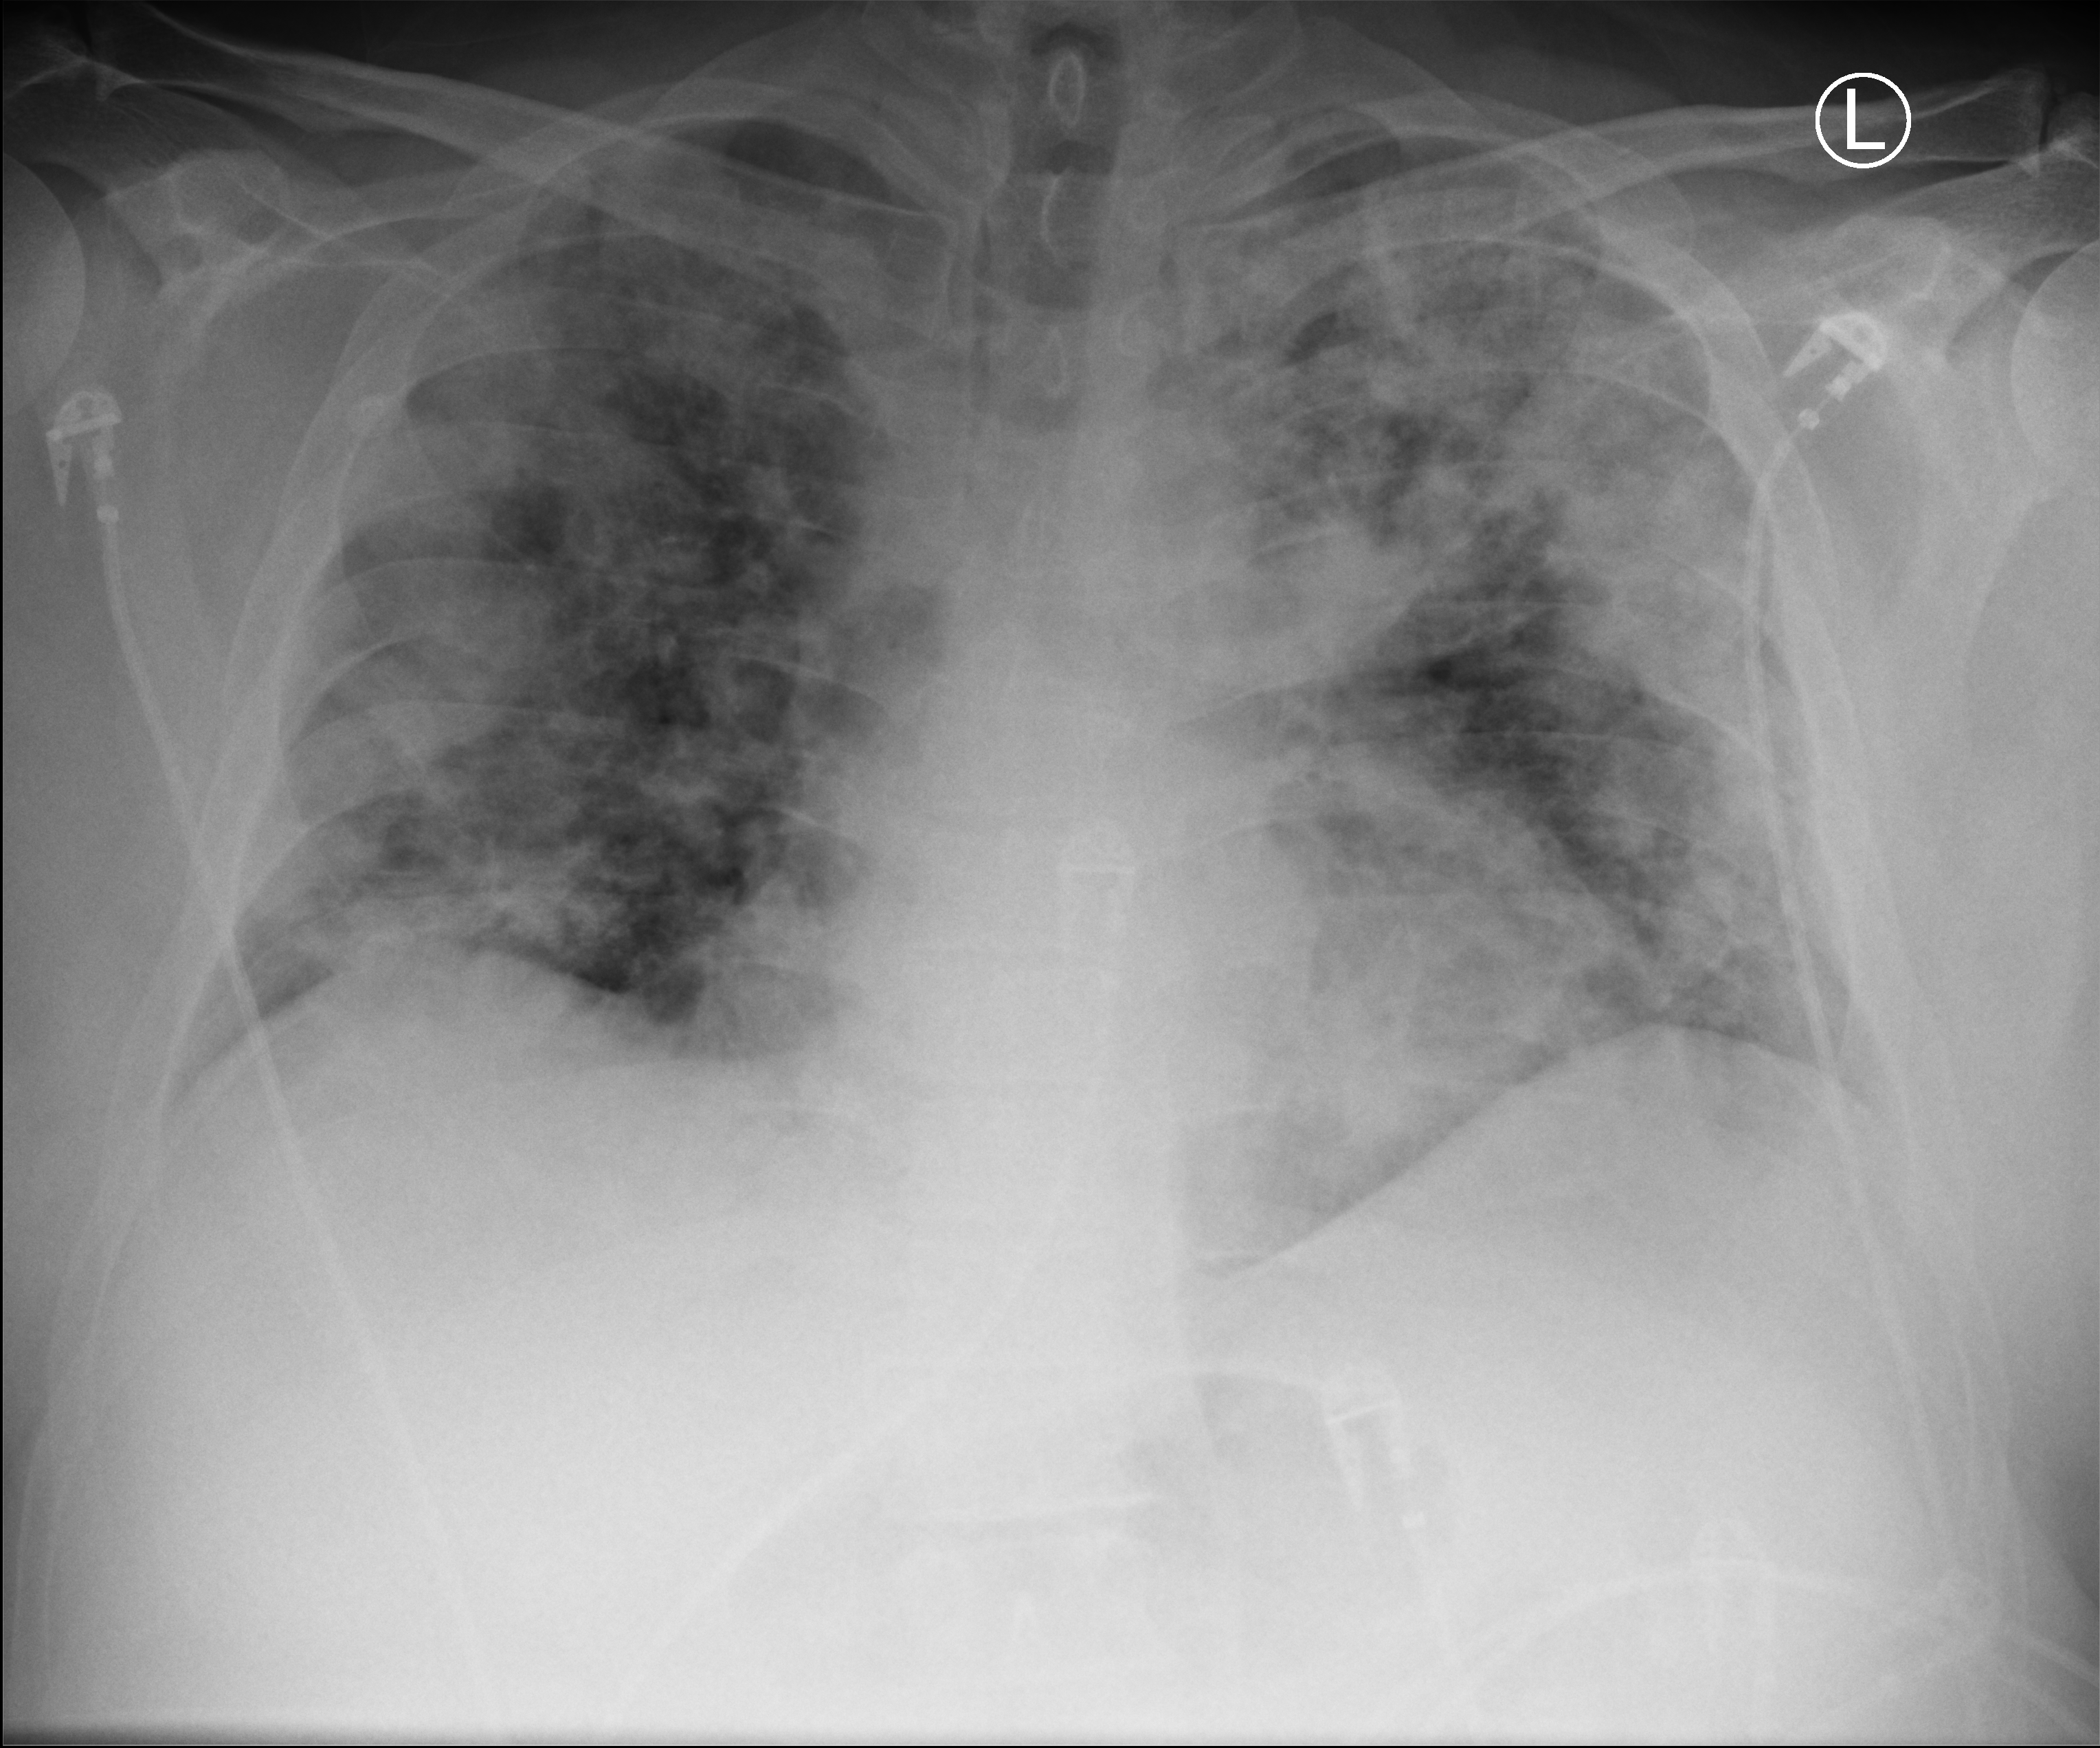
Bedside chest radiograph (computed radiography); anteroposterior (AP) projection. Male patient hospitalised with COVID-19, age 18–59 years.
From the hospital-stay record, not from the radiograph (when in the stay this image was taken is not recorded):
- length of hospital stay: 20 days
- admitted to intensive care during this hospital stay: yes
- chronic kidney disease (admission record): no